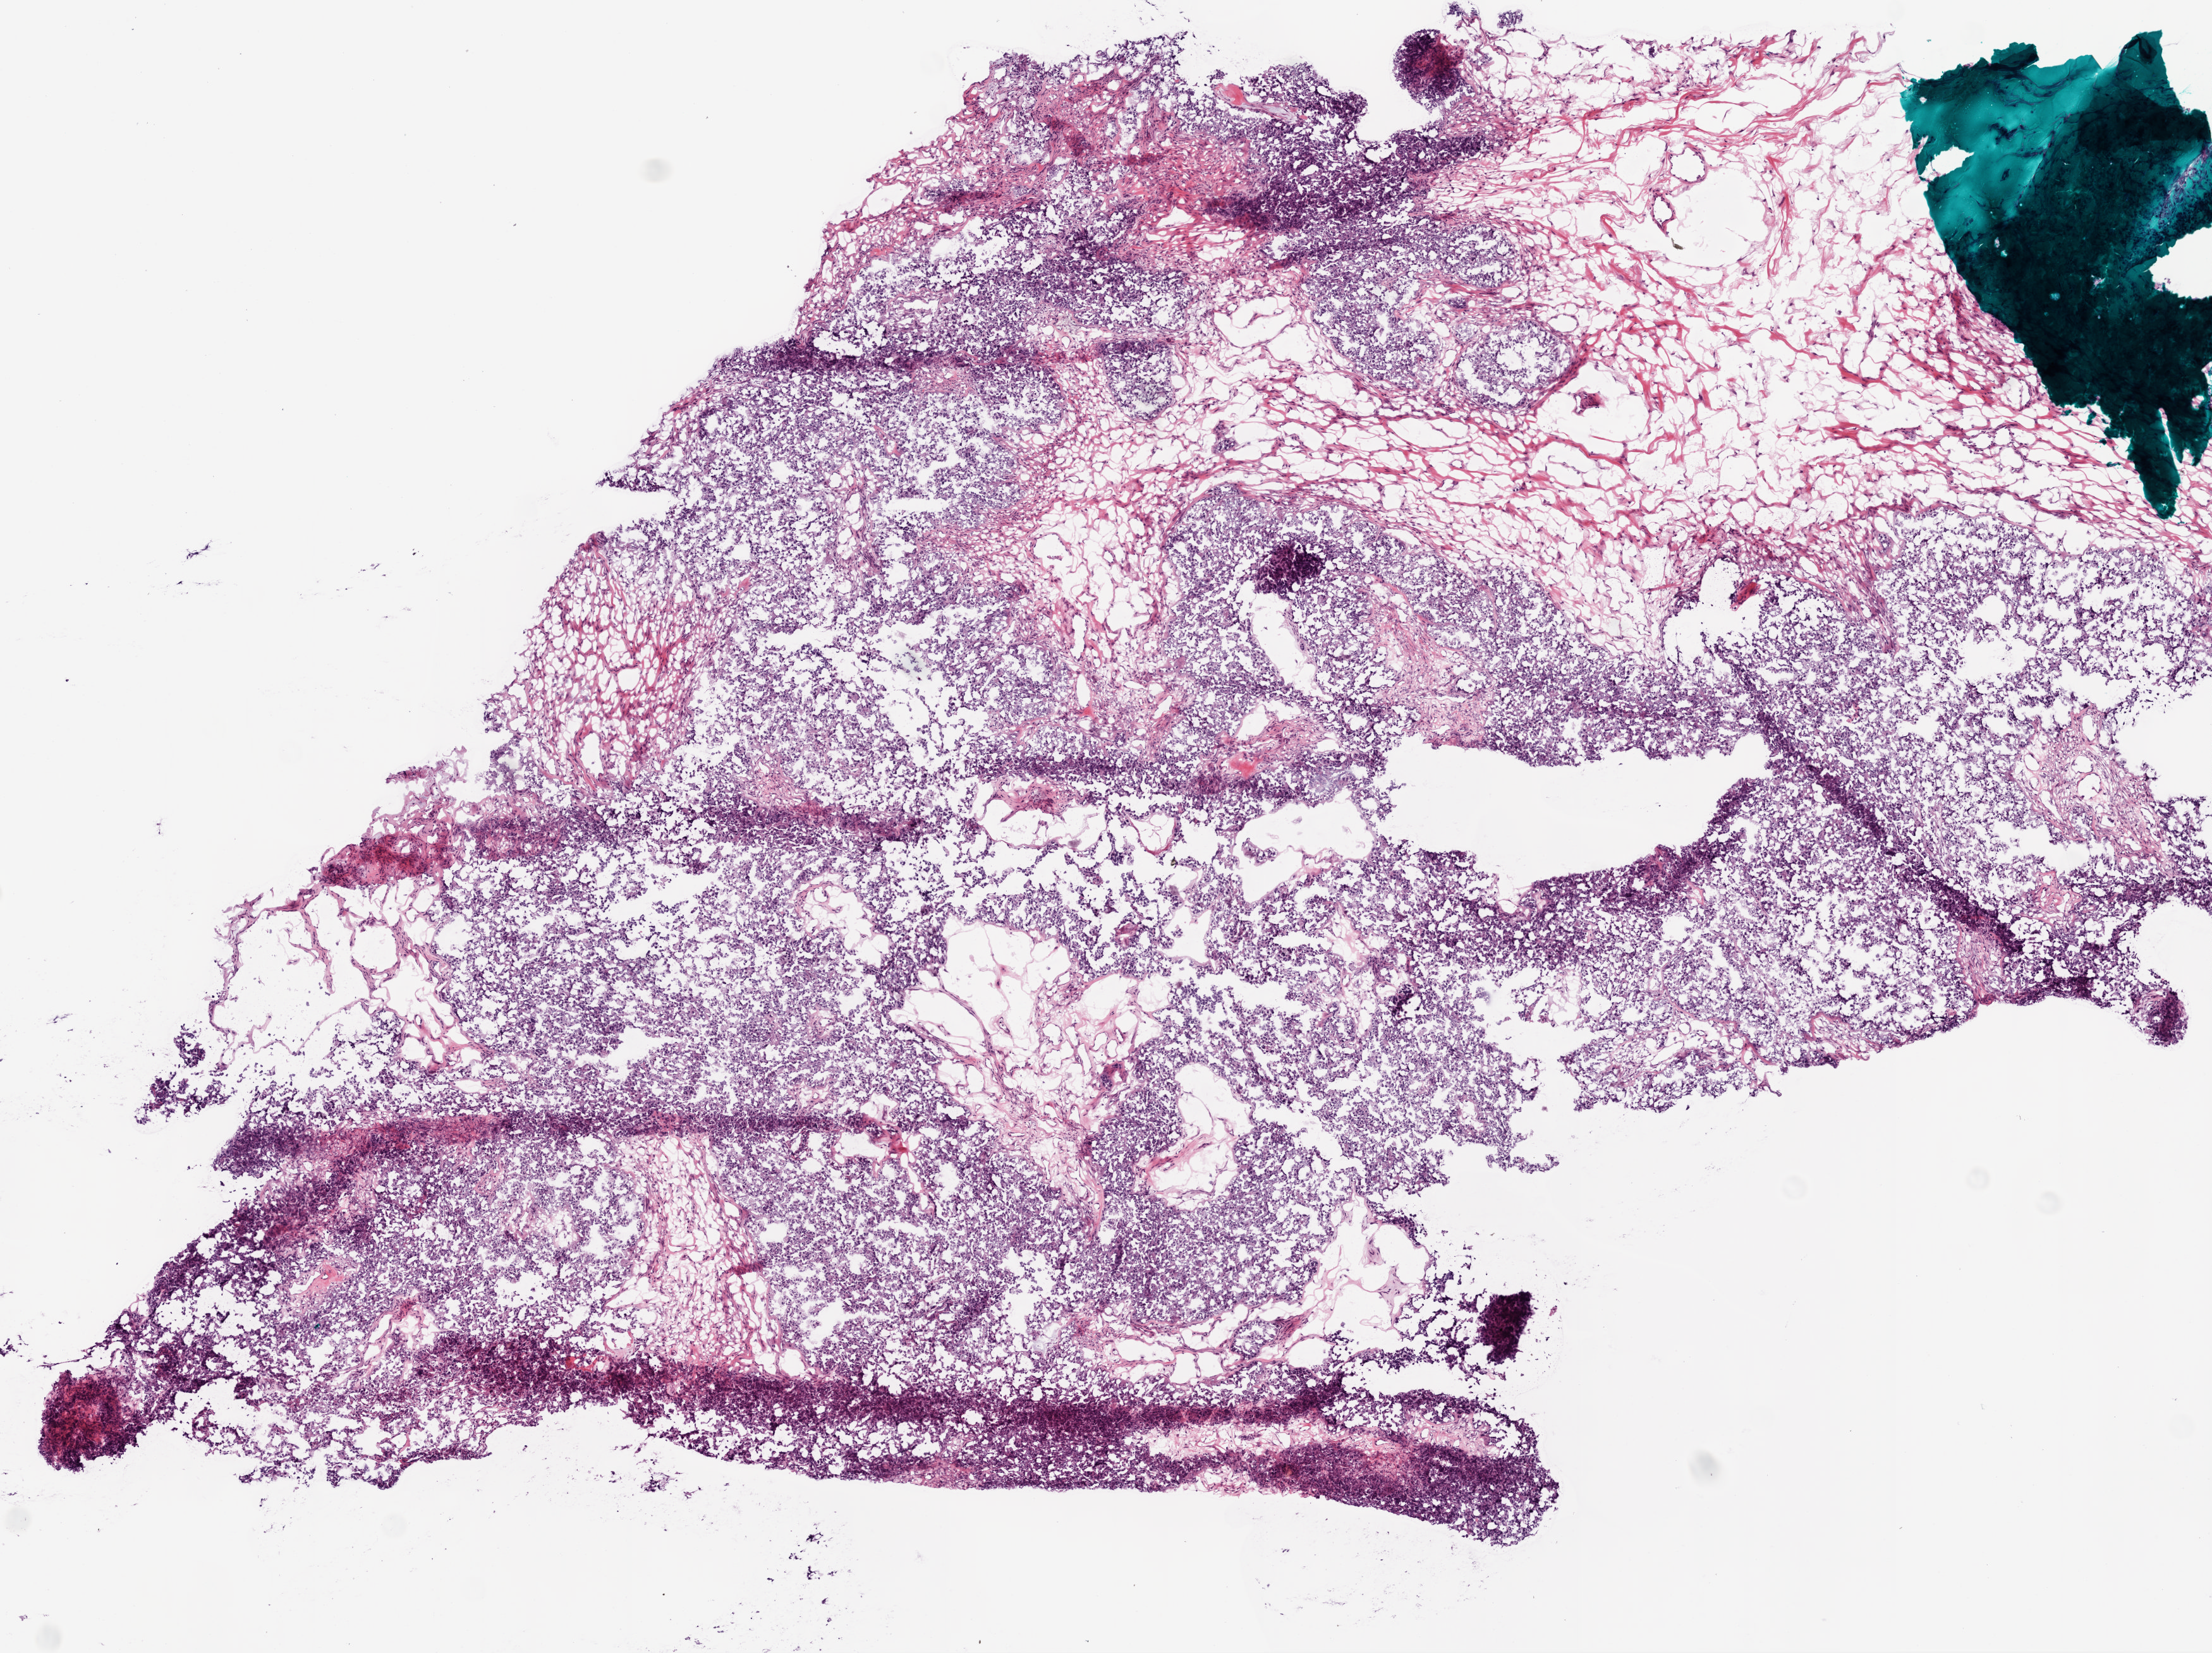
Digitized H&E tissue section (whole slide) — low-resolution overview of the scanned area, about 7.0 x 5.2 mm (slide scanned at 20x). Frozen section. Primary tumour sample from the ovary. Female patient; age at initial diagnosis 52 years. Histologic grade: G2 (moderately differentiated). Composition of this section per pathologist review: tumour cells 63%, tumour nuclei 80%, normal cells 42%, stromal cells 0%, necrosis 5%.
FIGO stage: IIIB. Laterality: bilateral. Diagnosis: Serous cystadenocarcinoma, NOS.